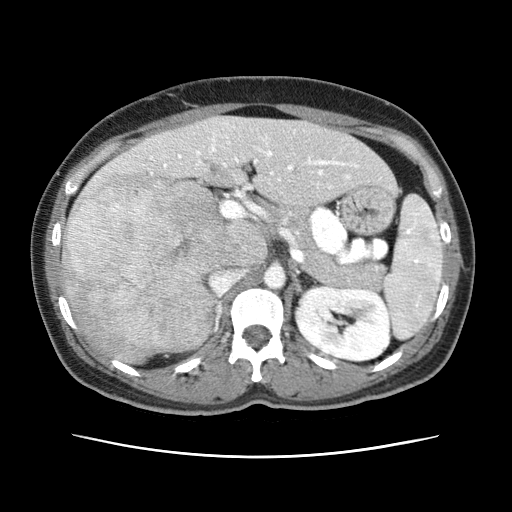
Contrast-enhanced abdominal CT (liver protocol), one axial slice; slice 30 of 79 in the series (ordered by position); soft-tissue window (W 400 / L 40 HU); 512 × 512 image matrix. Case-level facts recorded for this patient, not image findings: diagnosis: hepatocellular carcinoma (patient treated with transarterial chemoembolisation; whether this scan precedes or follows treatment is not stated here); TNM stage (as recorded): Stage-I; Child-Pugh class: A; tumour differentiation: moderately differentiated.
Structures marked on this image (semi-automatic segmentation, software-assisted and operator-edited):
- abdominal aorta: bounding box (x1, y1, x2, y2) in pixels: (264, 268, 286, 289)
- liver parenchyma outside the tumour (the mass and vessels are separate outlines, so this box may not span the whole liver): (62, 116, 384, 362)
- mass: (61, 171, 238, 360)
- liver vessels: (164, 138, 357, 179)